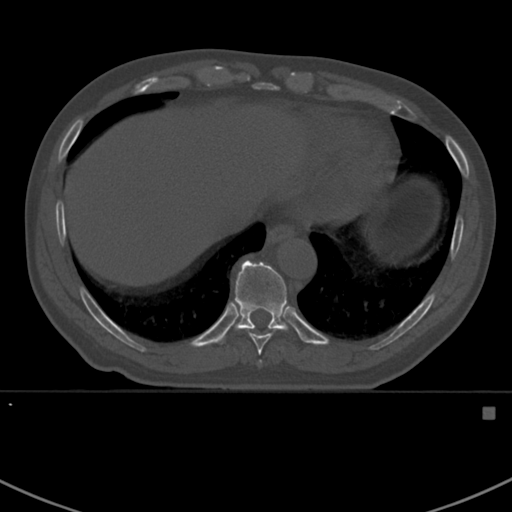
CT including the spine, one axial slice. Slice 374 of 412 in the series (ordered by position). Reconstruction kernel Br40s. 120 kVp. Bone window (W 1800 / L 400 HU). 512 × 512 image matrix, field of view 358 × 358 mm. Patient: male, 59 years. Case-level facts recorded for this patient, not image findings: primary cancer: prostate.
Annotated regions visible in this slice (semi-automatic segmentation, software-assisted and operator-edited):
- T10 vertebra: bounding box <217,261,296,345> (left, top, right, bottom; pixels)
- T8 vertebra: <259,362,261,364>
- T9 vertebra: <249,334,271,355>